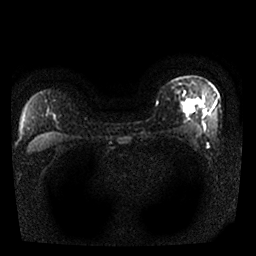
Breast MRI, one axial slice; slice 22 of 25 in the series (ordered by position); diffusion-weighted series; image 2 of 4 stored at this slice position (different b-values; order by instance number); 1.5 T; 4 mm slice thickness; 256 × 256 image matrix, field of view 320 × 320 mm. Female patient.
Annotated regions visible in this slice (expert manual segmentation):
- tumour on diffusion-weighted imaging: box from (x=185, y=101) to (x=198, y=109) px